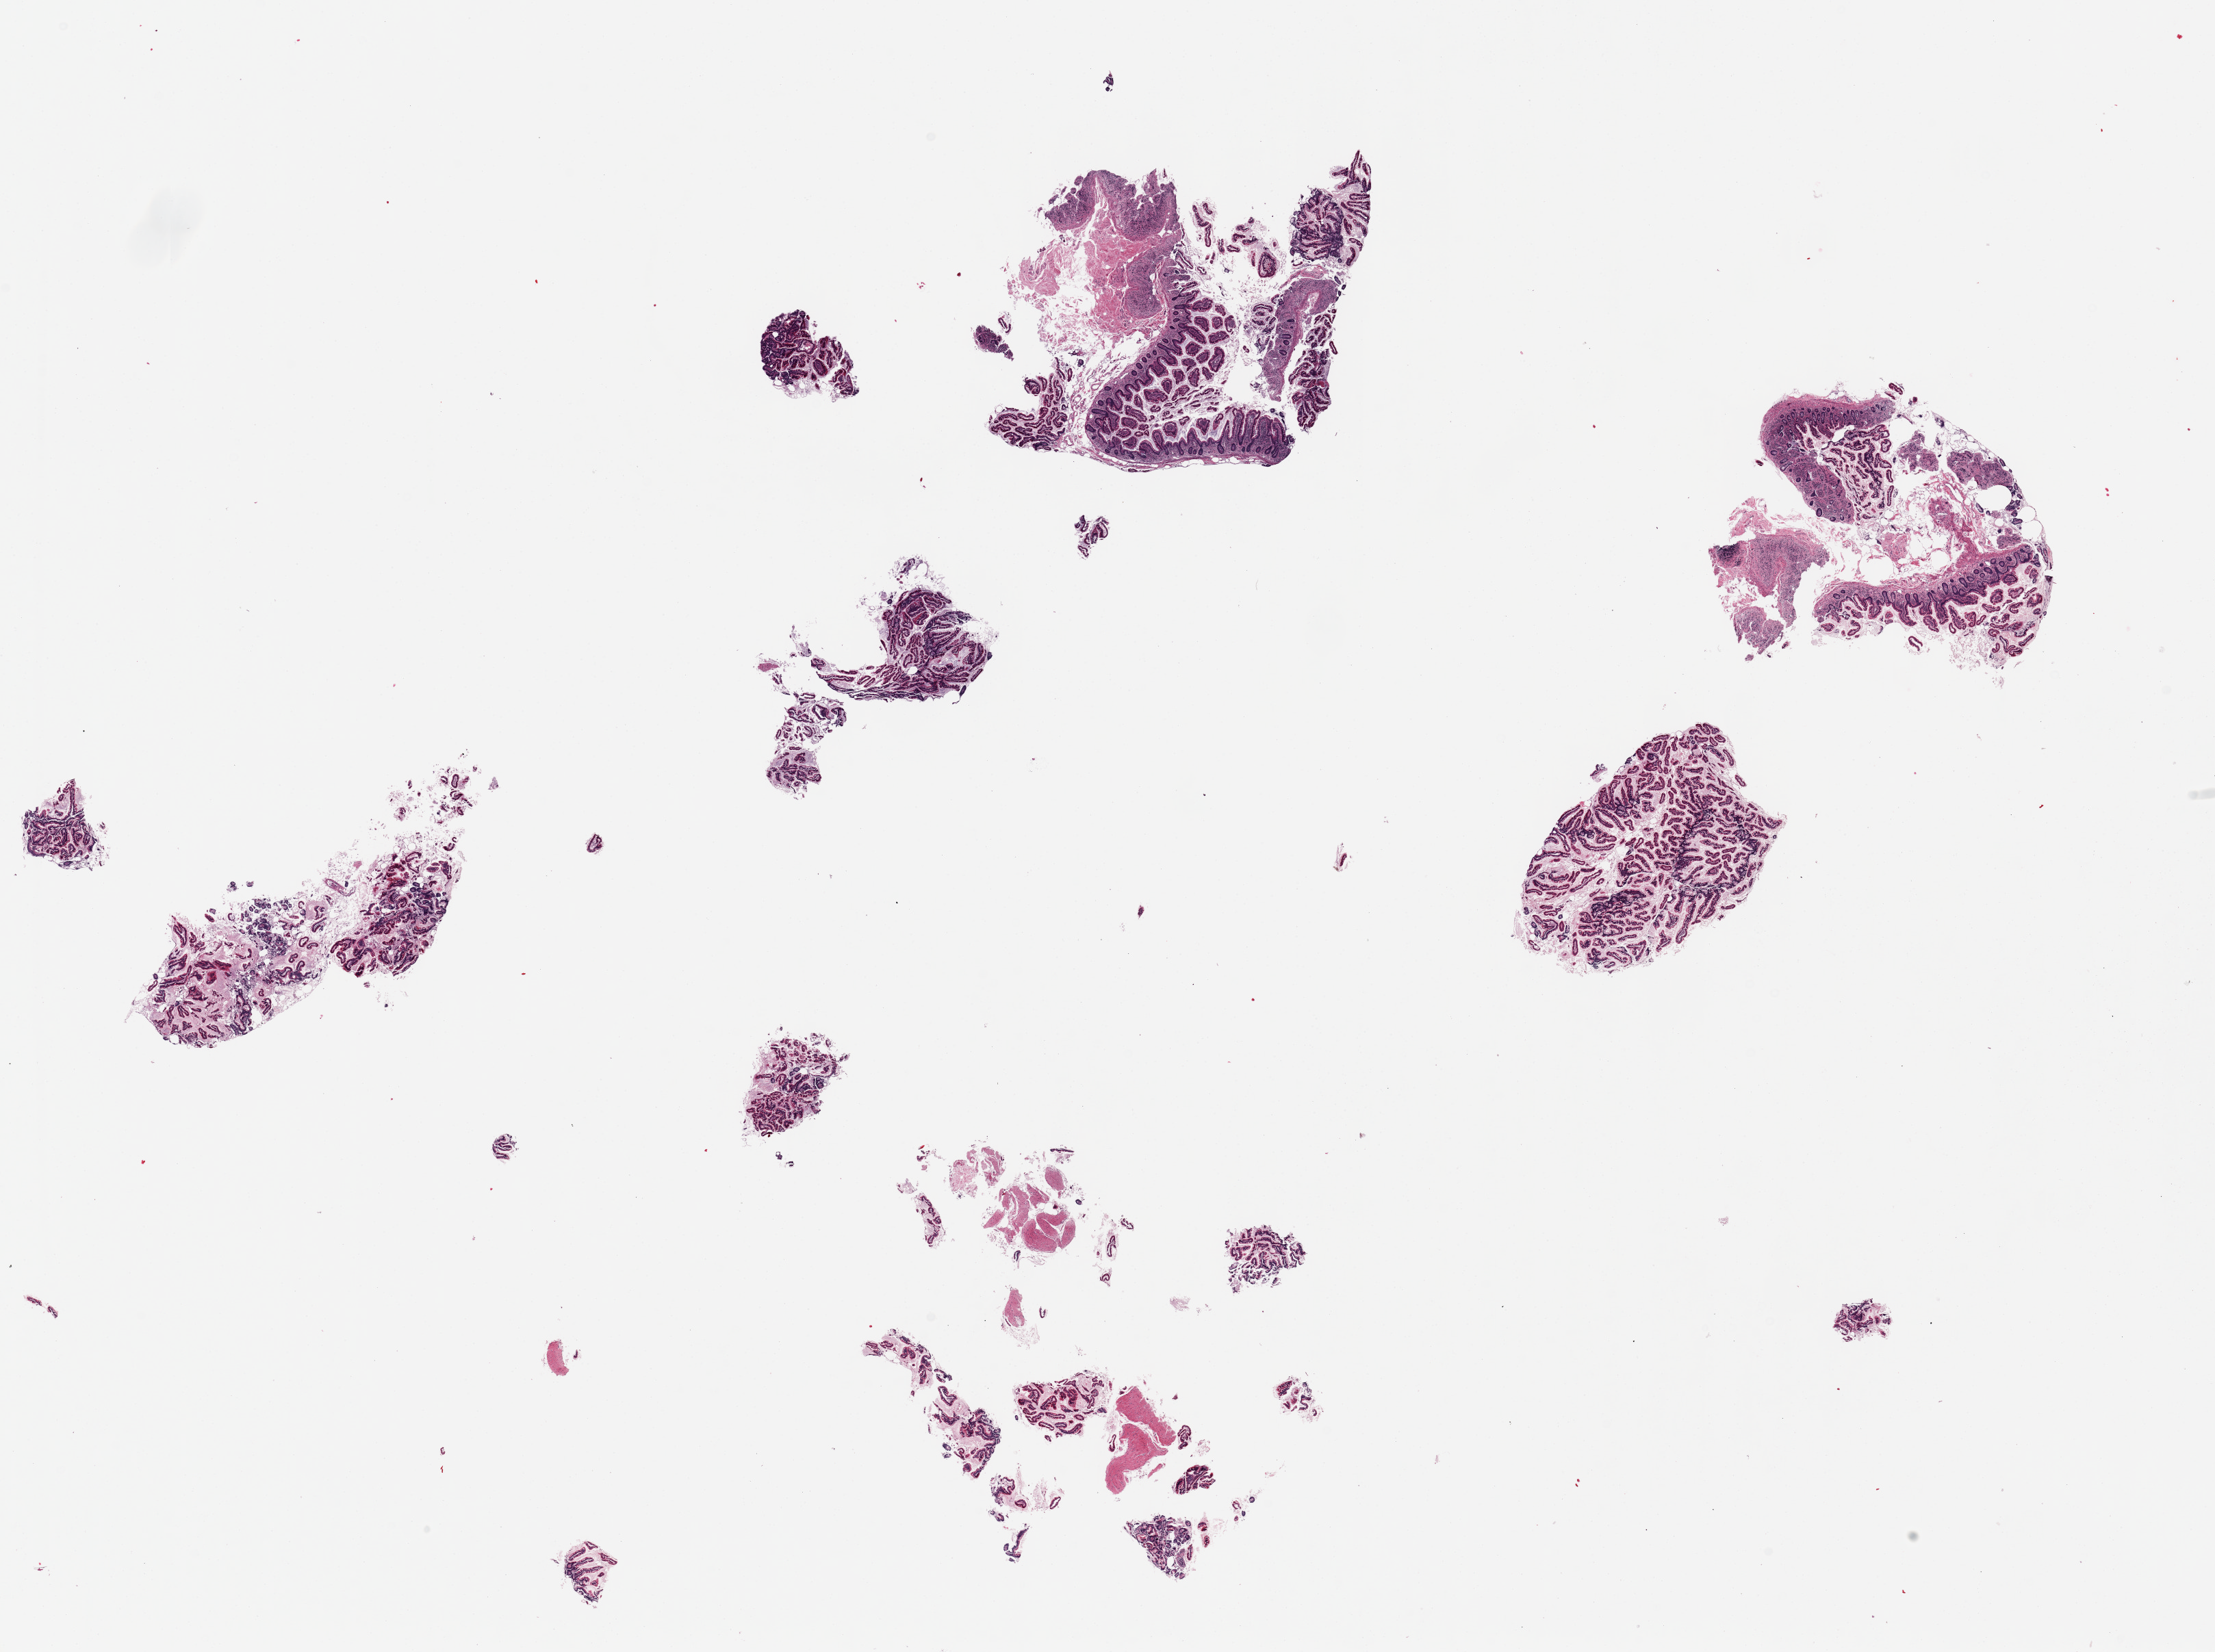
H&E whole-slide image — low-resolution overview of the scanned area, about 25.6 x 19.1 mm. PAXgene-fixed paraffin-embedded (PFPE) section. Section of ileum (target tissue). Tissue donor sample. Male donor.
- reviewer comment on this tissue sample: 6+ fragments, predominantly mucosa, partly autolyzed, and mucus, with single focus of degenerating lymphoid tissue